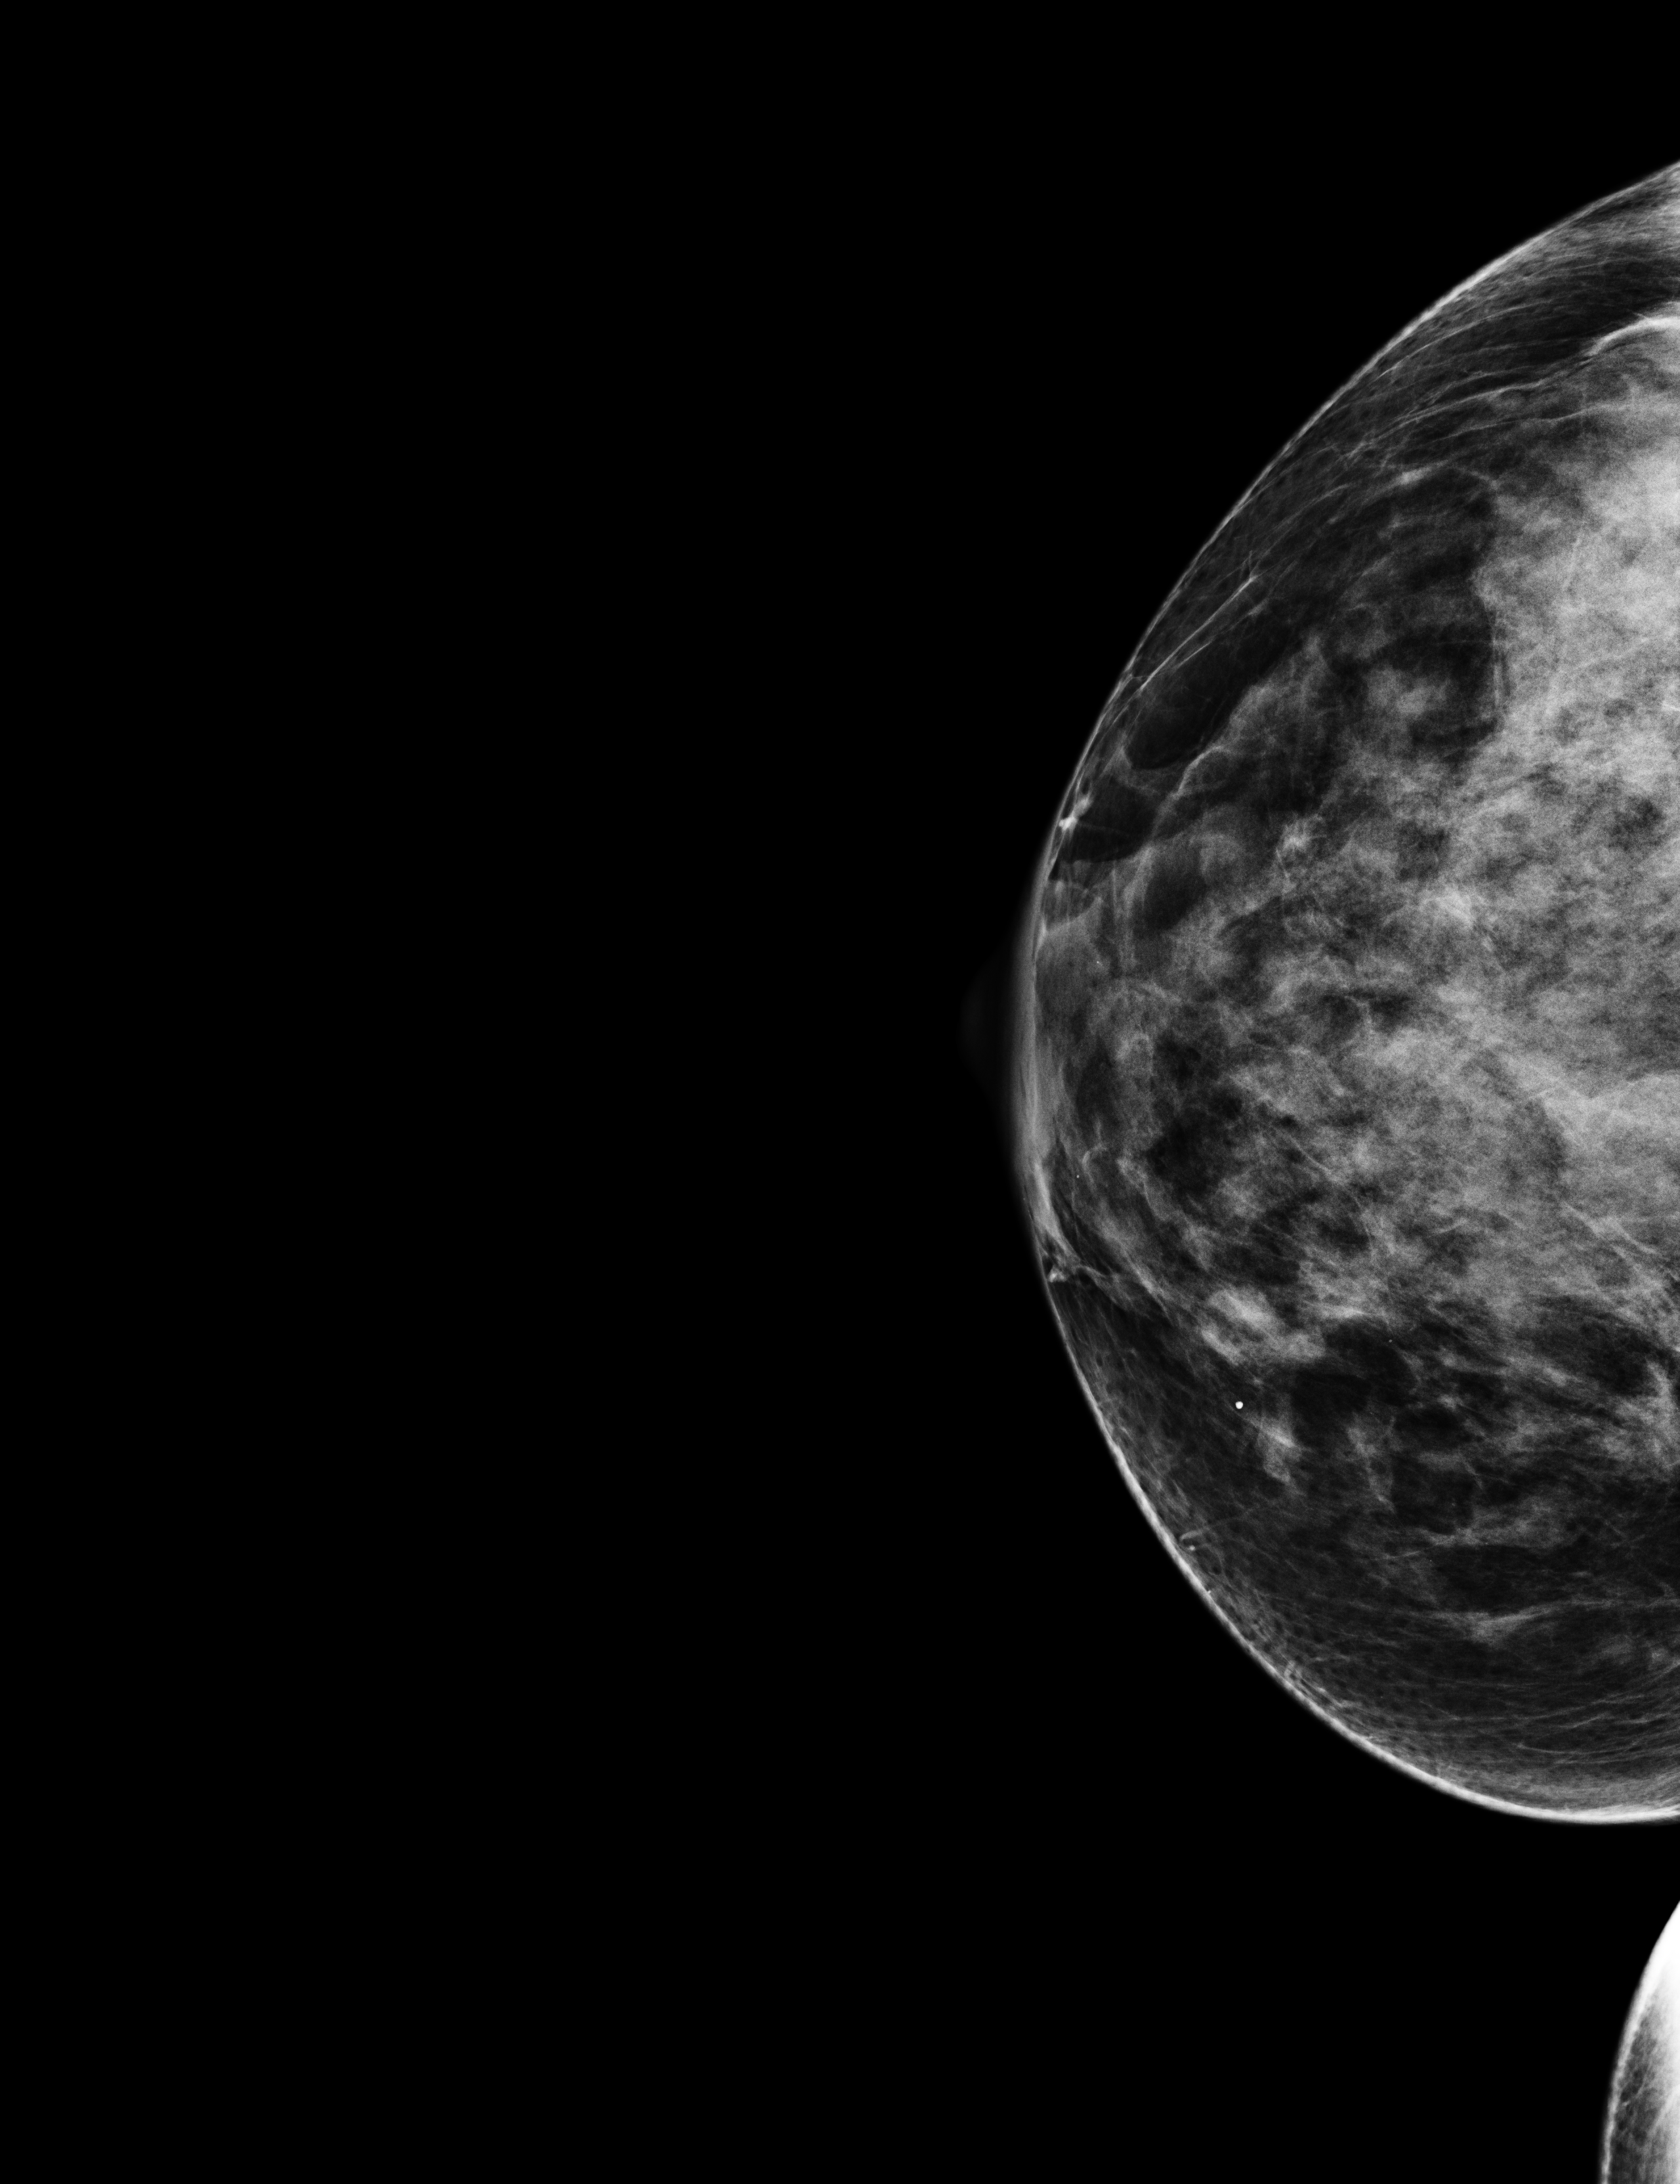
Annual screening mammography examination; compressed breast thickness 53 mm.
Image type: full-field digital mammogram. Breast: right. Projection: CC view.